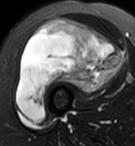
MRI of an extremity soft-tissue mass, one axial slice. T2-weighted fat-saturated. MR volume resampled by the dataset authors to the PET/CT grid (not the native acquisition matrix). 135 × 146 image matrix. Female patient. From the clinical record (not read from this slice): histological type: pleiomorphic undifferentiated sarcoma; grade: high; site of the primary tumour: right quadricep.
Outlined on this slice (expert contour drawn on MRI and transferred to this co-registered scan by the dataset authors):
- gross tumour volume including surrounding oedema: bounding box (x1, y1, x2, y2) in pixels: (16, 18, 123, 124)
- gross tumour volume (mass): (16, 18, 123, 124)